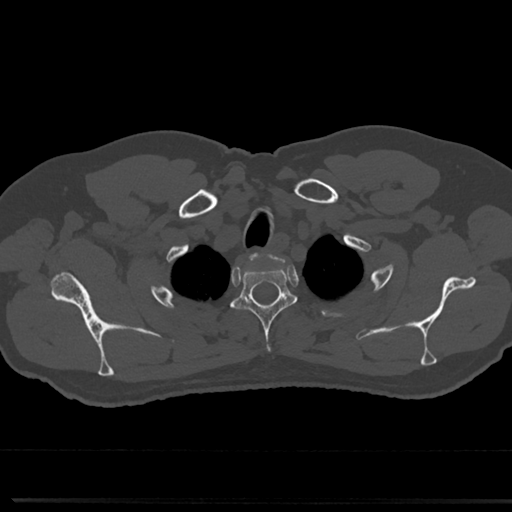
CT including the spine, one axial slice. Position 635 of 817 along the scan axis. Reconstruction kernel Br40s/3. 120 kVp. Bone window (W 1800 / L 400 HU). 0.5 mm slice thickness. 512 × 512 image matrix. Male patient, age 61 years. From the clinical record (not read from this slice): primary cancer: prostate.
Annotated regions visible in this slice (semi-automatic segmentation, software-assisted and operator-edited):
- T2 vertebra: box from (x=234, y=260) to (x=295, y=355) px
- T3 vertebra: (x=300, y=312)–(x=310, y=324)